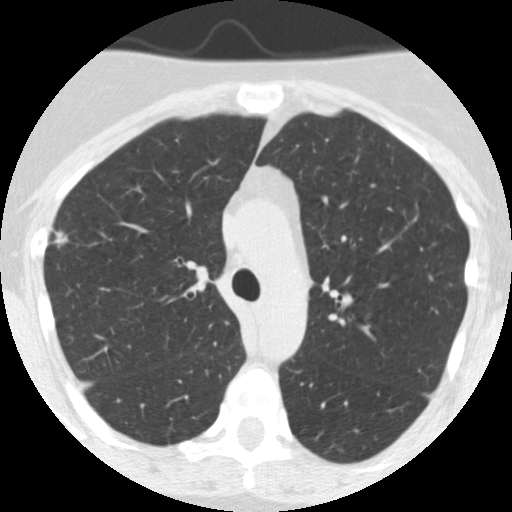
Chest CT (low-dose screening protocol), one axial image; first (baseline) screen; lung window (W 1500 / L -600 HU); 2.5 mm slice thickness; slice 170 of 249 in the series; 512 × 512 image matrix. Female, age 55 years at enrolment.
Expert reader's lesion annotation, bounding box (x1, y1, x2, y2) in pixels: (31, 219, 83, 266). Screening reader's record for this exam (one nodule recorded; not confirmed to be the boxed lesion): non-calcified nodule or mass ≥4 mm, right upper lobe, 7 × 7 mm, spiculated (stellate) margins, soft tissue attenuation. Official screen result: positive, change unspecified: nodule(s) >= 4 mm or enlarging nodule(s), mass(es), or other non-specific abnormalities suspicious for lung cancer. Lung cancer was diagnosed 1018 days after this screen: bronchiolo-alveolar adenocarcinoma, NOS, right upper lobe, moderately differentiated (G2), stage IIA (AJCC 6th edition), 13 mm at pathology.